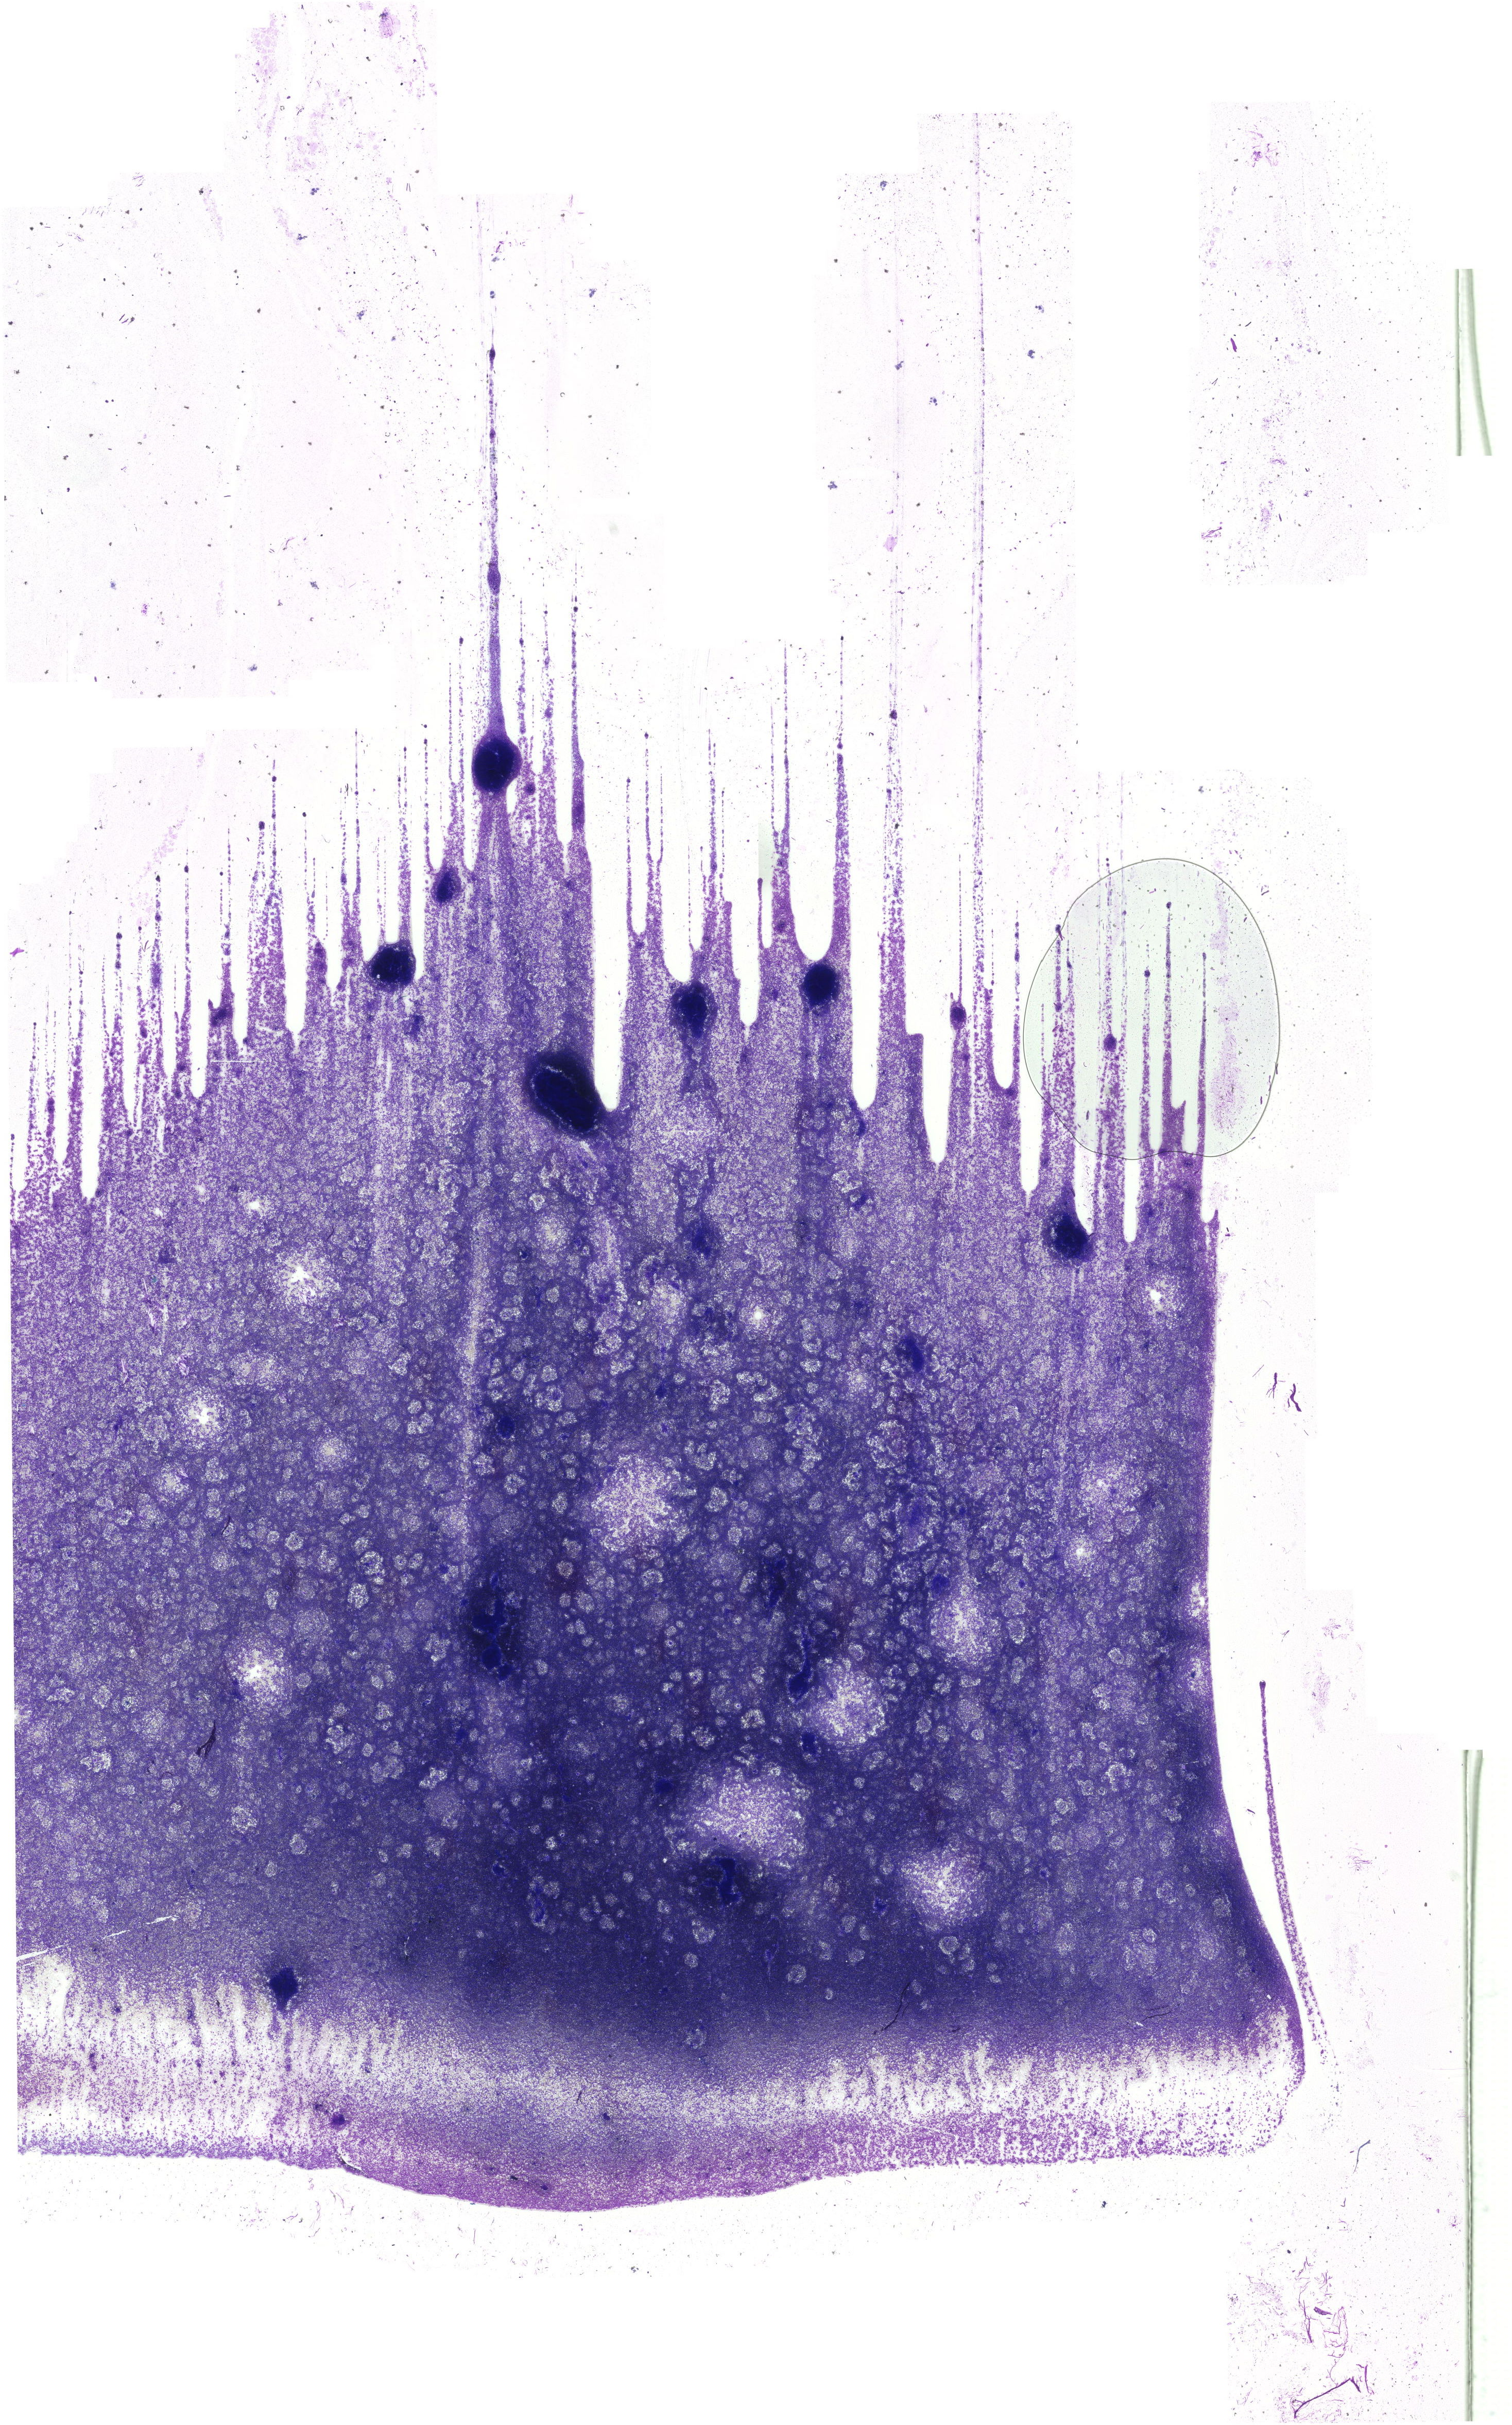
May-Grünwald-Giemsa (MGG)-stained marrow aspirate smear (whole slide) — shown as a low-resolution overview of the whole scanned area (about 20.8 x 33.4 mm). Female patient.
Diagnosis: Chronic Phase Chronic Myeloid Leukemia, BCR-ABL1 Positive.